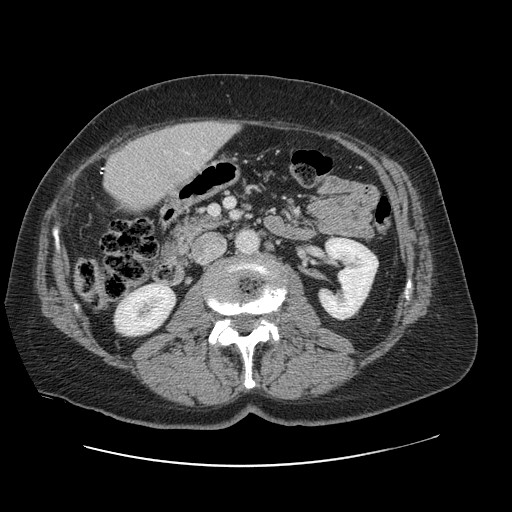
Contrast-enhanced abdominal CT, one axial slice; position 25 of 138 along the scan axis; 120 kVp; intravenous contrast given; soft-tissue window (W 400 / L 40 HU); 2.5 mm slice thickness; 512 × 512 image matrix, field of view 402 × 402 mm. Male patient, age 71 years. Case-level facts recorded for this patient, not image findings: diagnosis: colorectal cancer liver metastases, imaged before liver resection; multiple liver metastases: no; largest metastasis: 3.3 cm; chemotherapy before resection: no.
Outlined on this slice (outlined manually by an expert reader):
- liver: bounding box <105,121,236,212> (left, top, right, bottom; pixels)
- planned liver remnant (the part of the liver to remain after resection): <103,134,178,211>